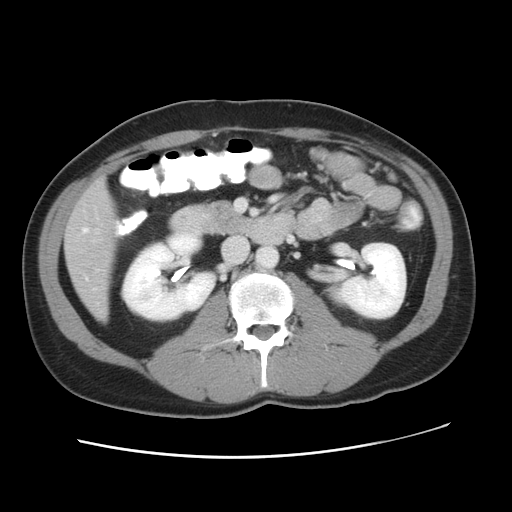
Contrast-enhanced abdominal CT, one axial slice; position 19 of 49 along the scan axis; reconstruction kernel STANDARD; 120 kVp; intravenous contrast given; soft-tissue window (W 400 / L 40 HU); 5 mm slice thickness; 512 × 512 image matrix. Male patient, age 41 years. From the clinical record (not read from this slice): diagnosis: colorectal cancer liver metastases, imaged before liver resection; multiple liver metastases: yes; largest metastasis: 0.7 cm; chemotherapy before resection: yes.
Annotated regions visible in this slice (outlined manually by an expert reader):
- hepatic veins: box from (x=82, y=227) to (x=97, y=280) px
- liver: (x=67, y=181)–(x=115, y=320)